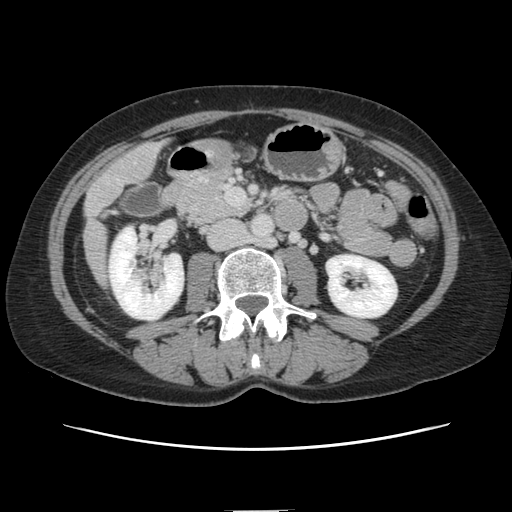
Contrast-enhanced abdominal CT, one axial slice. Slice 38 of 141 in the series (ordered by position). Intravenous contrast given. Soft-tissue window (W 400 / L 40 HU). 2.5 mm slice thickness. 512 × 512 image matrix. Female patient, age 63 years. Case-level facts recorded for this patient, not image findings: diagnosis: colorectal cancer liver metastases, imaged before liver resection; multiple liver metastases: yes; largest metastasis: 3.2 cm; disease in both lobes: yes.
Annotated regions visible in this slice (manually delineated by an expert):
- liver: box from (x=85, y=143) to (x=161, y=284) px